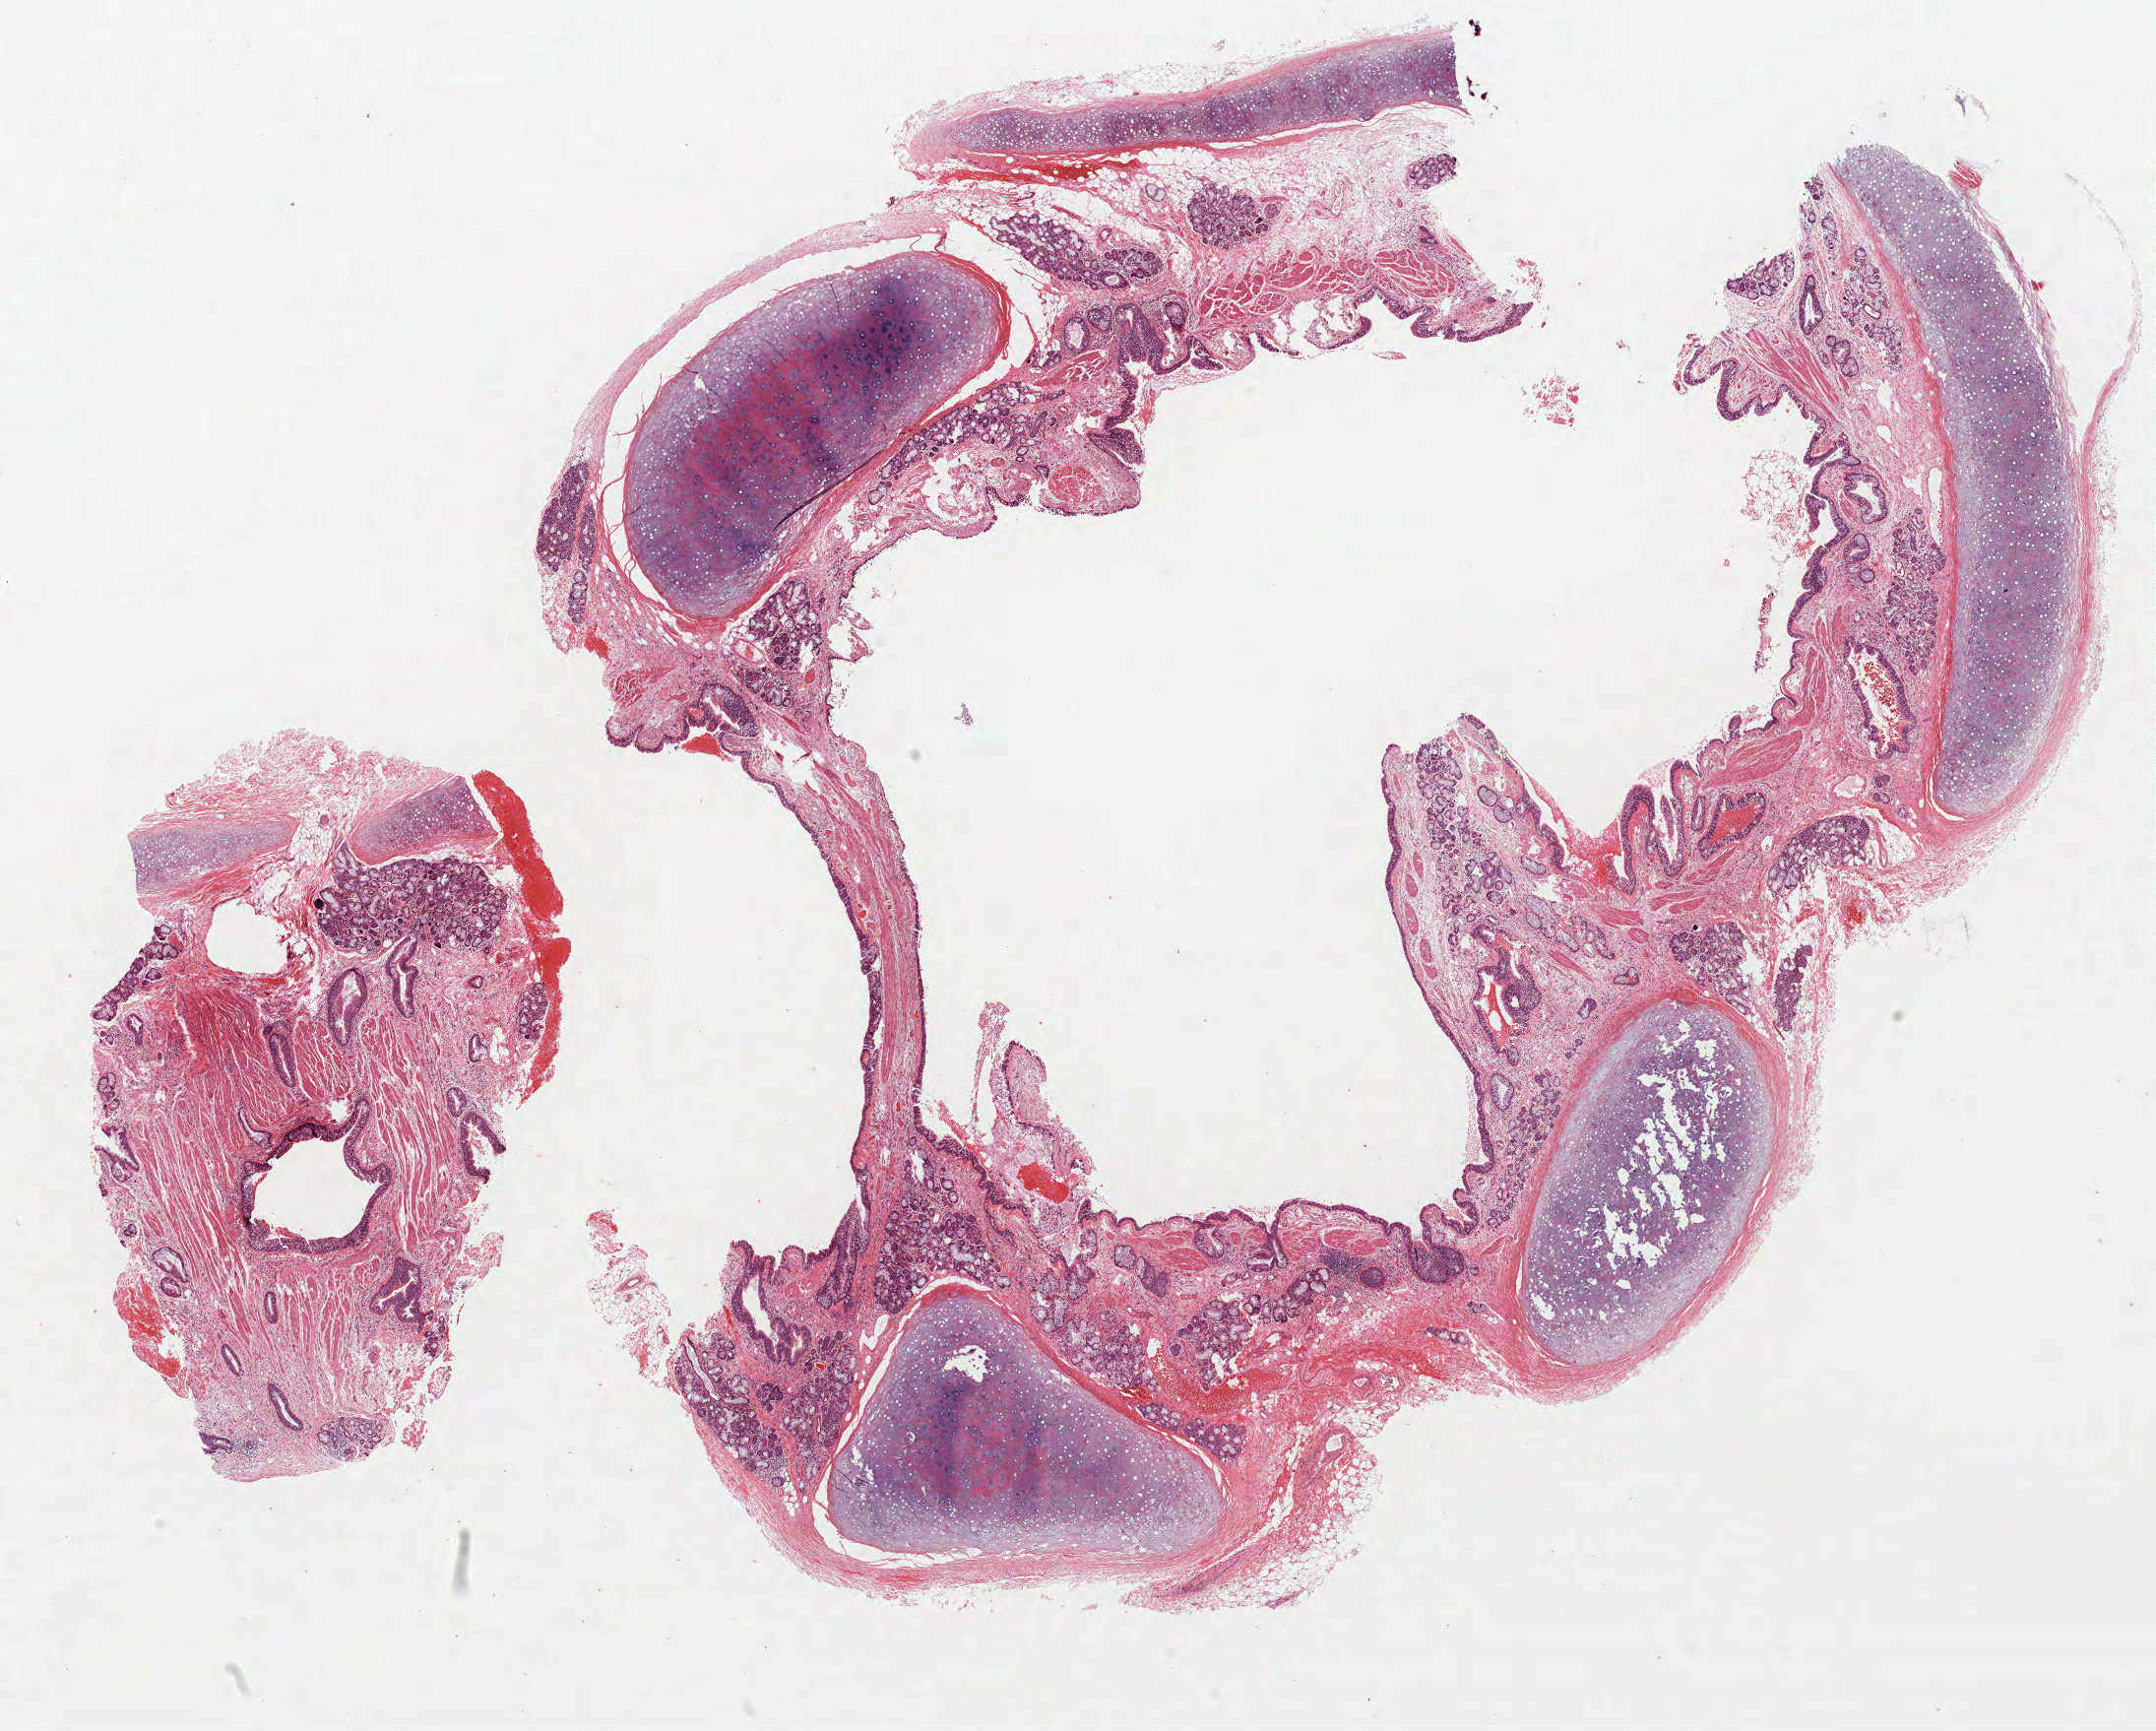
Hematoxylin and eosin (H&E) stained whole-slide image — low-resolution overview of the scanned area, about 17.5 x 14.1 mm (slide scanned at 40x); formalin-fixed paraffin-embedded (FFPE) section; lung tissue. Male patient, aged 57 at enrolment. Current smoker at enrolment. Grade: well differentiated (G1).
Primary tumour location (clinical record): left upper lobe. Stage (AJCC 6th edition): IA. Participant's lung-cancer diagnosis: Adenocarcinoma, NOS. Tumour size (pathology): 30 mm.